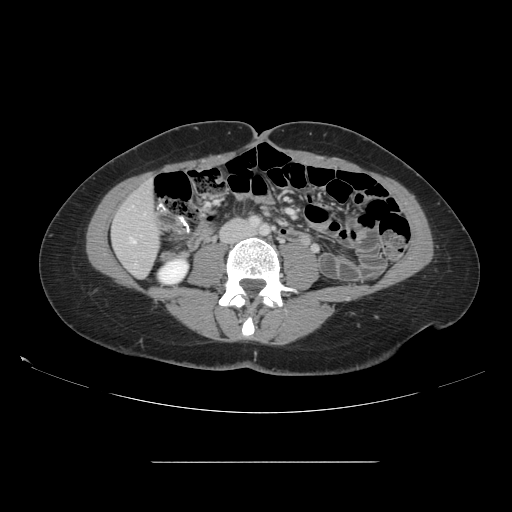
Contrast-enhanced abdominal CT, one axial slice. Slice 29 of 151 in the series (ordered by position). Intravenous contrast given. Soft-tissue window (W 400 / L 40 HU). 2.5 mm slice thickness. 512 × 512 image matrix, field of view 421 × 421 mm. Female patient, age 46 years. From the clinical record (not read from this slice): diagnosis: colorectal cancer liver metastases, imaged before liver resection; multiple liver metastases: yes; largest metastasis: 3 cm; disease in both lobes: yes.
Structures marked on this image (expert manual segmentation):
- hepatic veins: box from (x=131, y=239) to (x=135, y=243) px
- liver: (x=113, y=184)–(x=159, y=277)
- planned liver remnant (the part of the liver to remain after resection): (x=113, y=184)–(x=160, y=277)